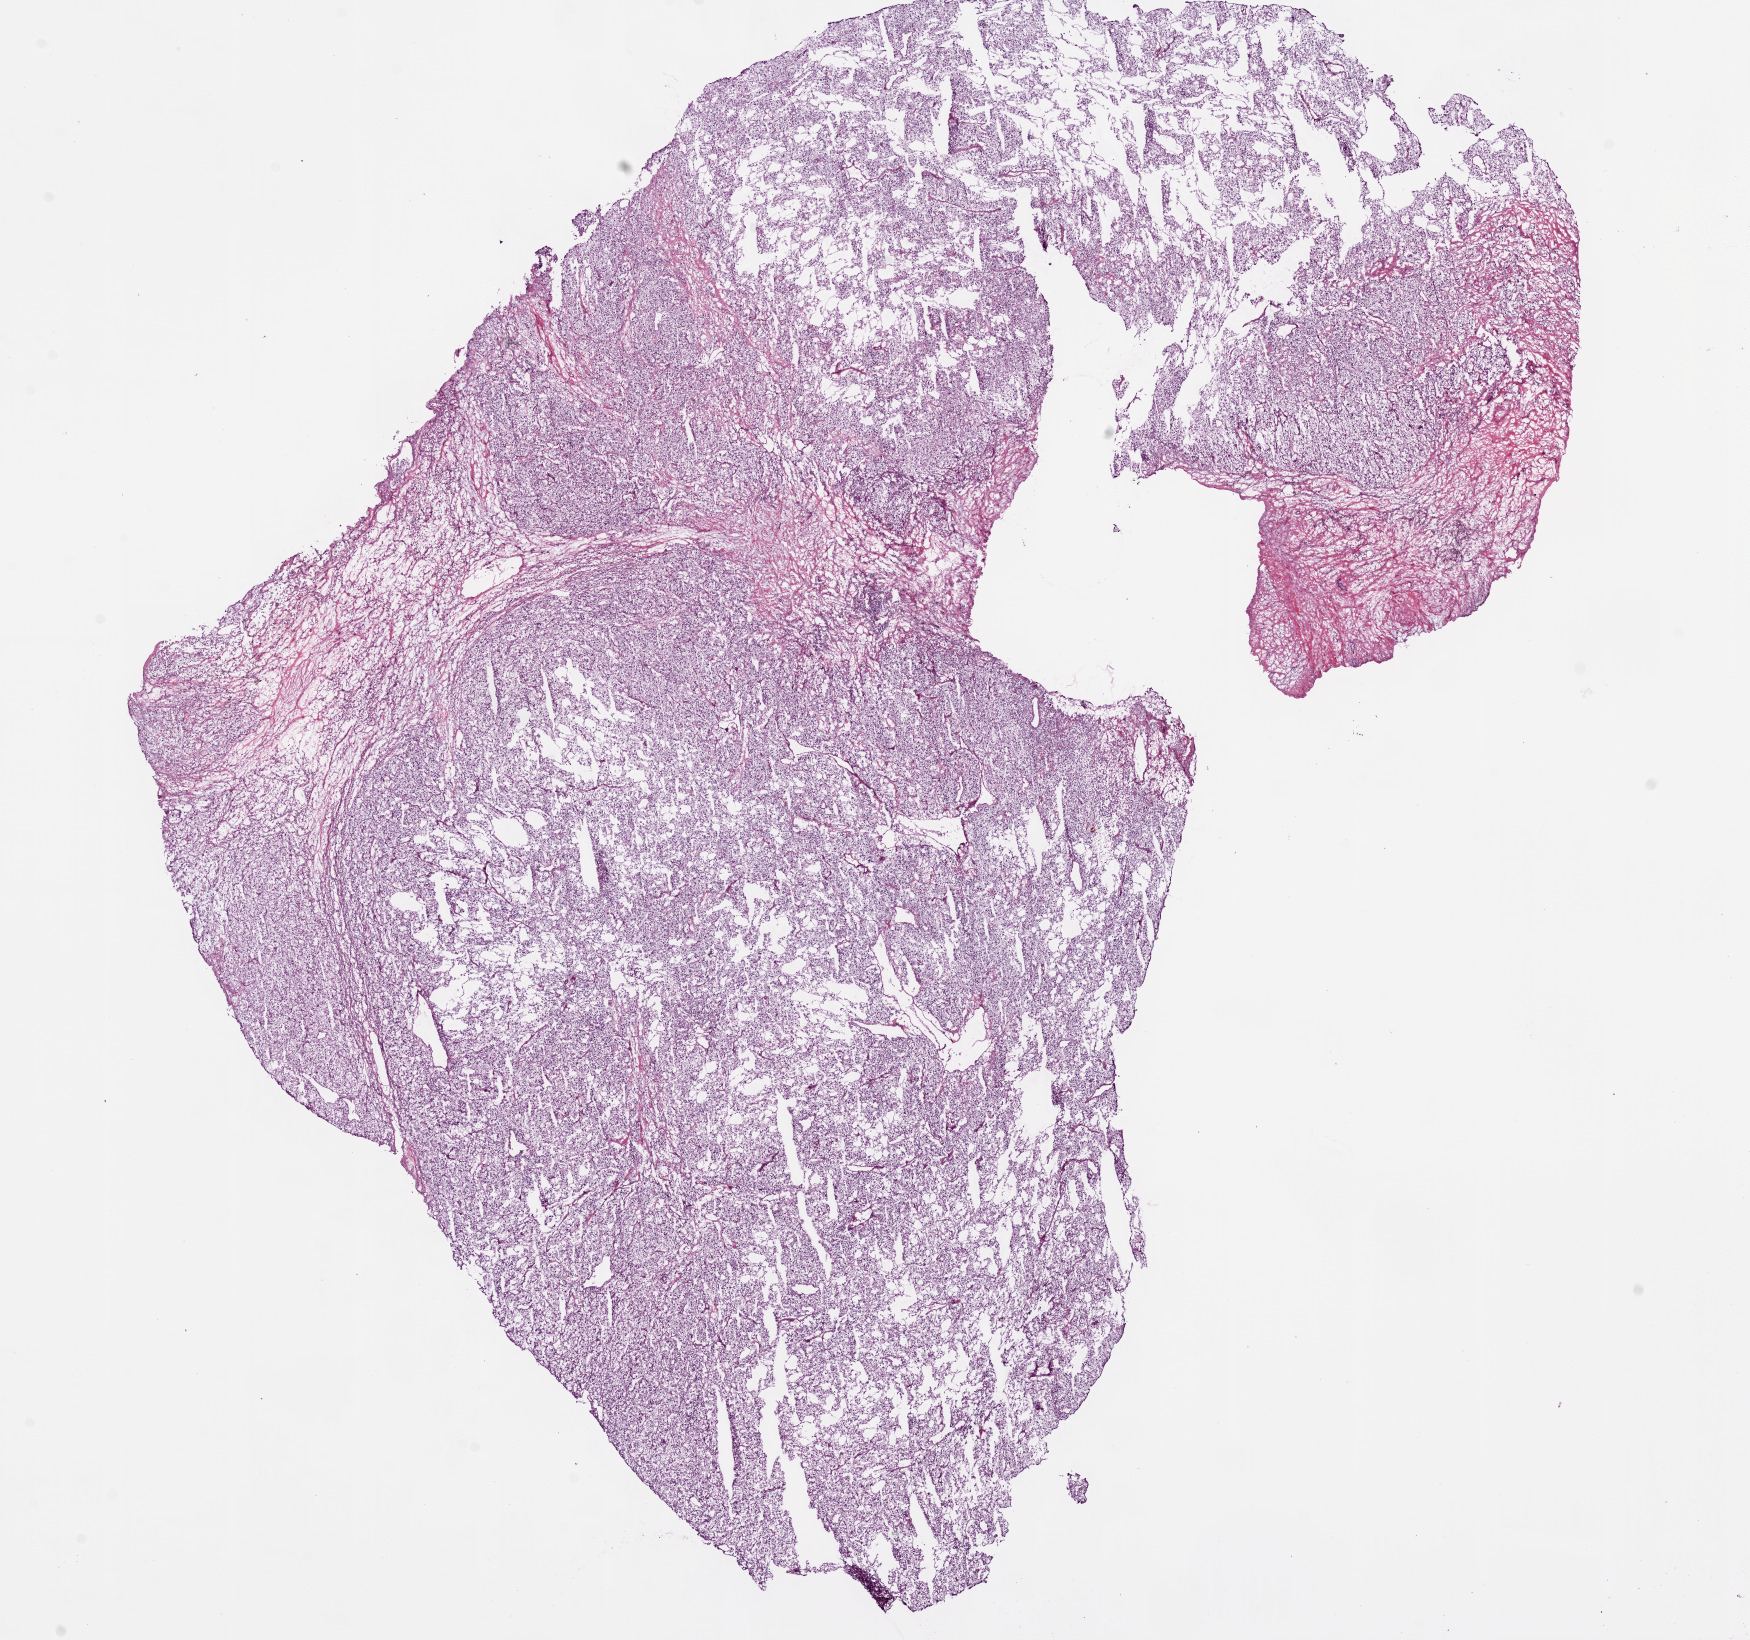
Whole-slide histology image, H&E-stained, low-resolution overview of the scanned area, about 14.0 x 13.2 mm, frozen section, primary tumour sample from the kidney. Male, age 56 years at initial diagnosis. Slide review estimates, as recorded: tumour cells 90%, tumour nuclei 90%.
Pathologic diagnosis: Clear cell adenocarcinoma, NOS.